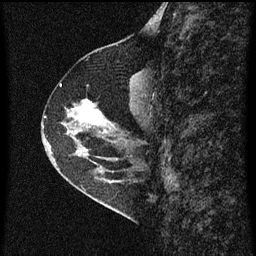
Breast MRI (dynamic contrast-enhanced), one sagittal slice. Slice 26 of 60 in the series (ordered by position). Dynamic contrast-enhanced series, image 2 of 3 at this slice position (ordered by acquisition). 1.5 T. TE 4.2 ms, TR 8 ms. 2 mm slice thickness. 256 × 256 image matrix, field of view 180 × 180 mm. Patient: female, 56 years.
Structures marked on this image (semi-automatic segmentation, software-assisted and operator-edited):
- analysis volume of interest (the breast-tissue region the enhancement analysis was run in; not a lesion): box from (x=49, y=98) to (x=110, y=159) px
- tumour enhancement mask (voxels above the 70 % enhancement threshold inside the analysis volume of interest): (x=76, y=100)–(x=103, y=125)